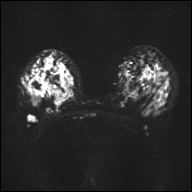
Breast MRI, one axial slice. Slice 24 of 32 in the series (ordered by position). Diffusion-weighted series; image 2 of 4 stored at this slice position (different b-values; order by instance number). 1.5 T. 4 mm slice thickness. 192 × 192 image matrix, field of view 360 × 360 mm. Female patient.
Structures marked on this image (outlined manually by an expert reader):
- tumour on diffusion-weighted imaging: bounding box [x1, y1, x2, y2] px = [43, 76, 73, 112]